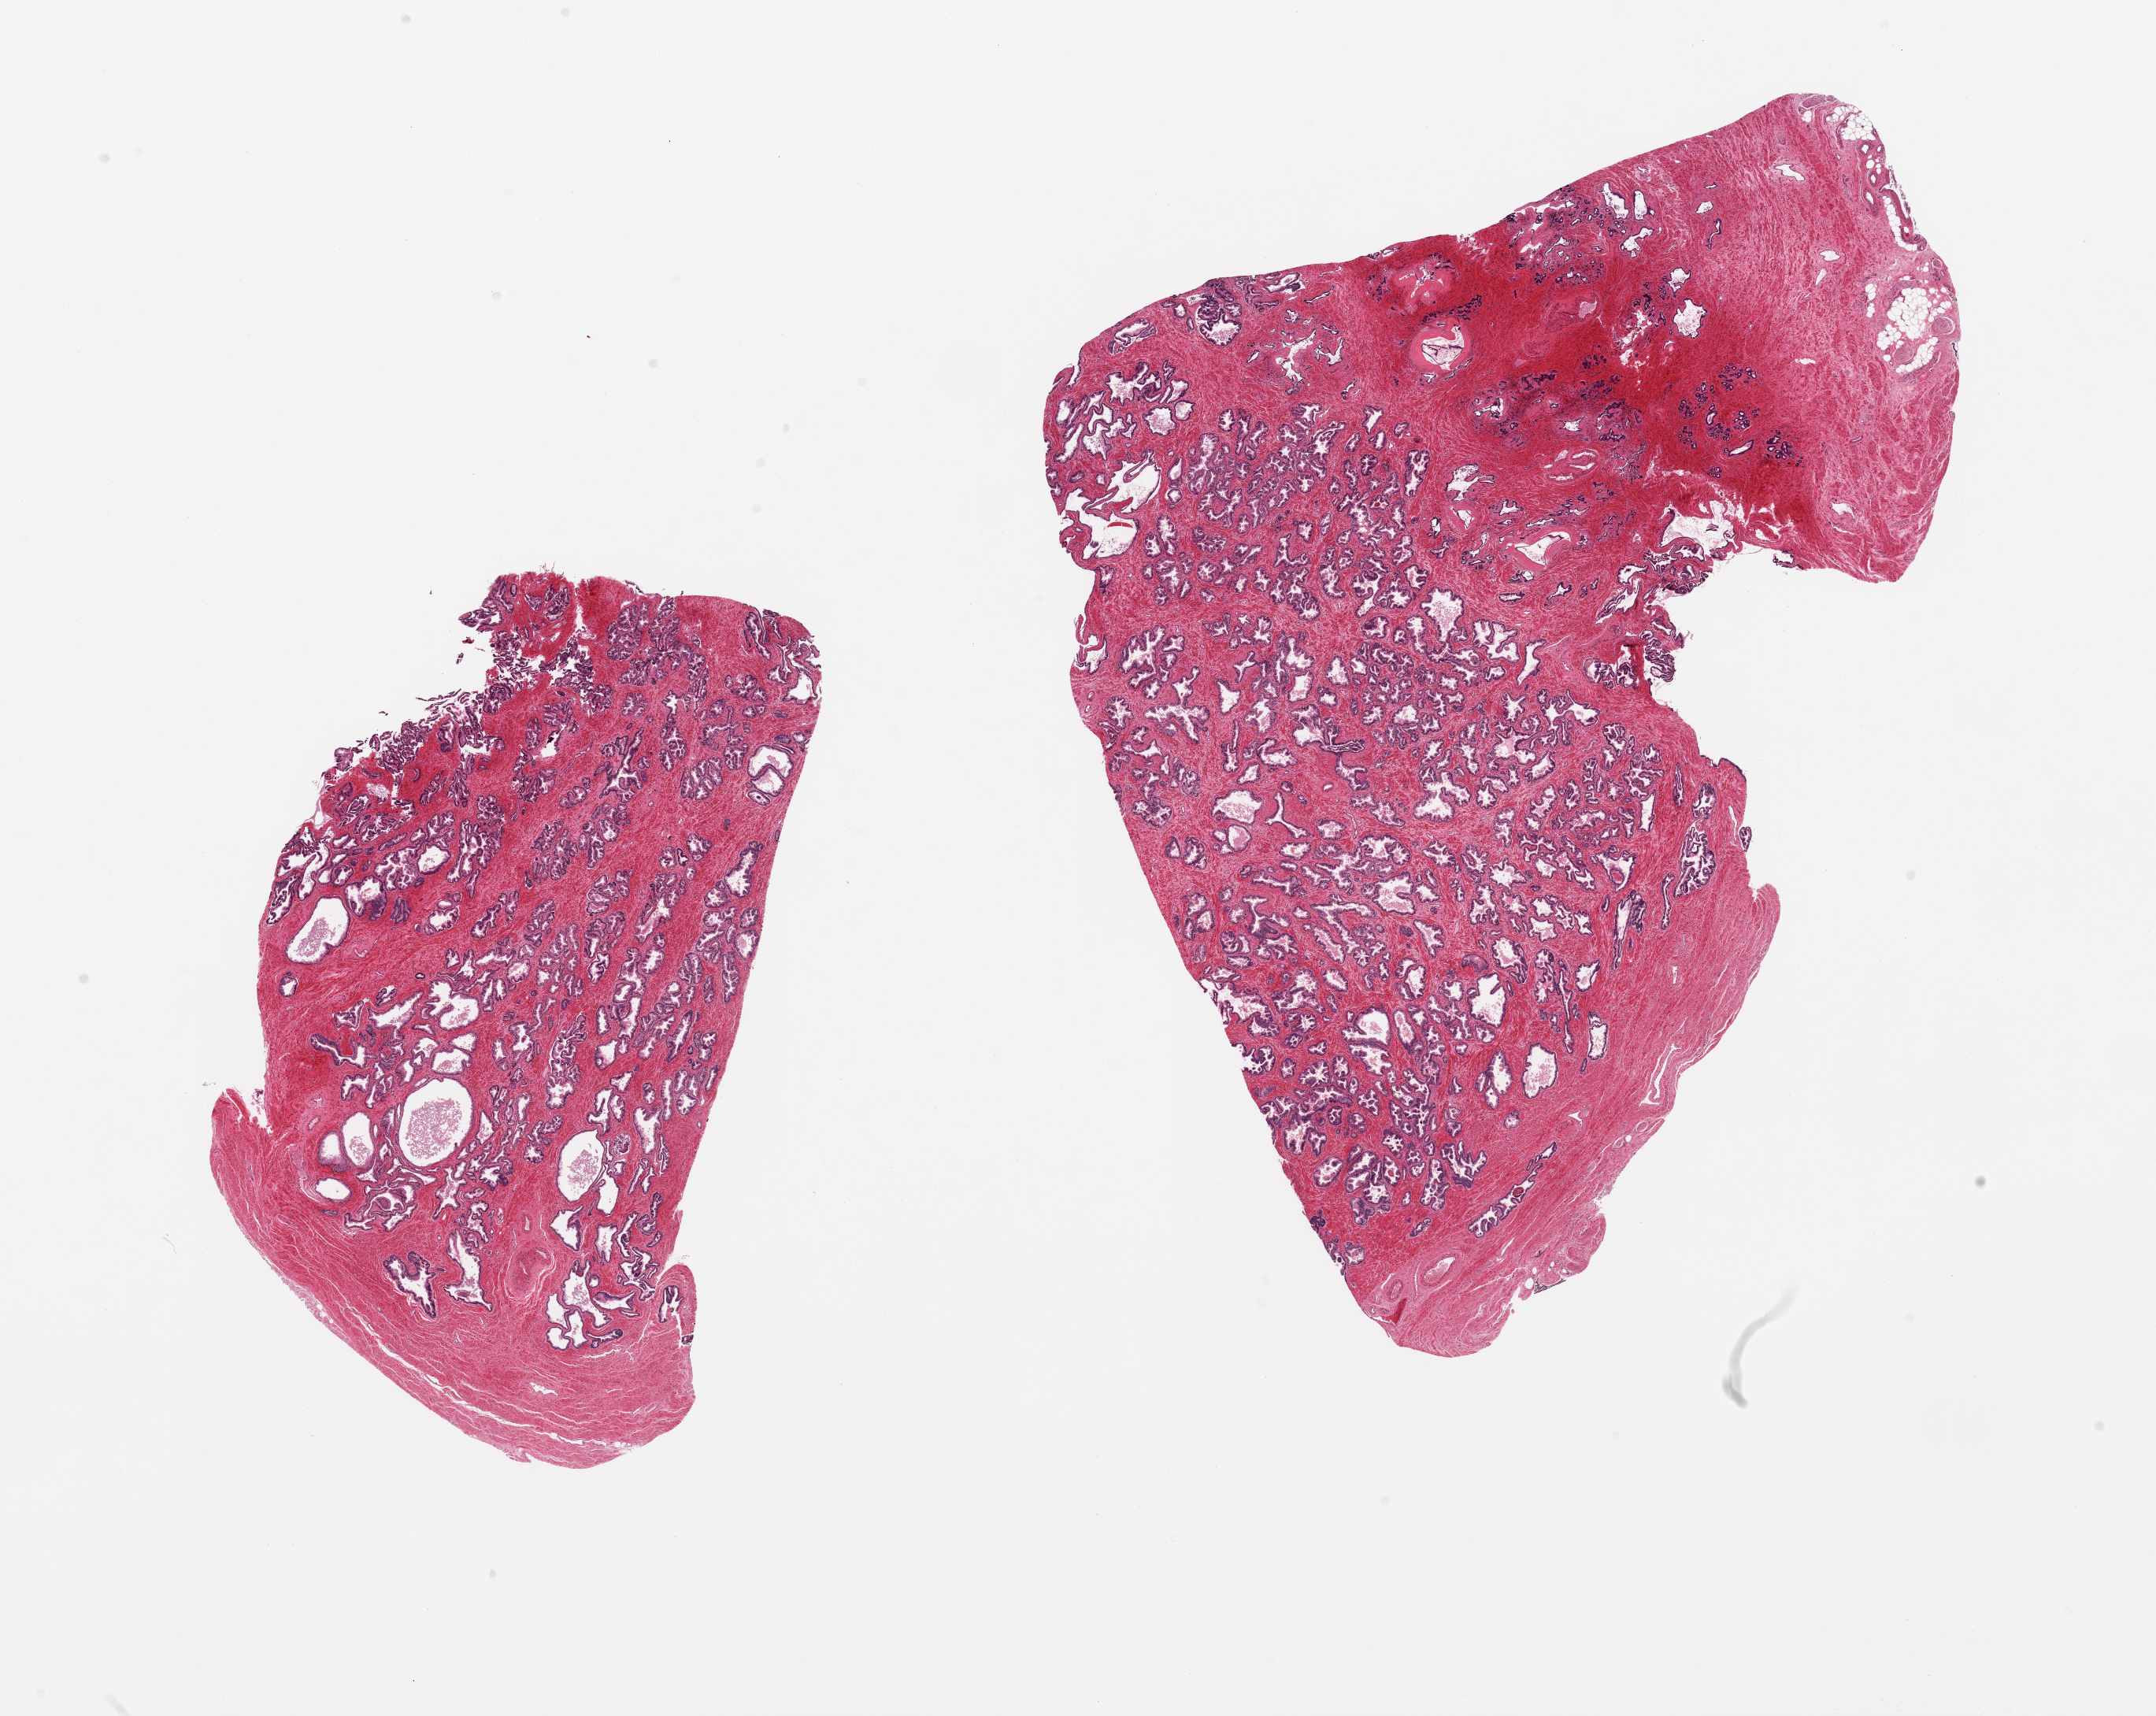
Whole-slide image, hematoxylin and eosin (H&E) stain, a low-resolution overview of the entire scanned area, about 21.7 x 17.2 mm, PAXgene-fixed, paraffin-embedded tissue, section of prostate (target tissue), tissue donor sample. Donor sex: male.
- reviewer comment on this tissue sample: 2 pieces; well preserved glandular and stromal components